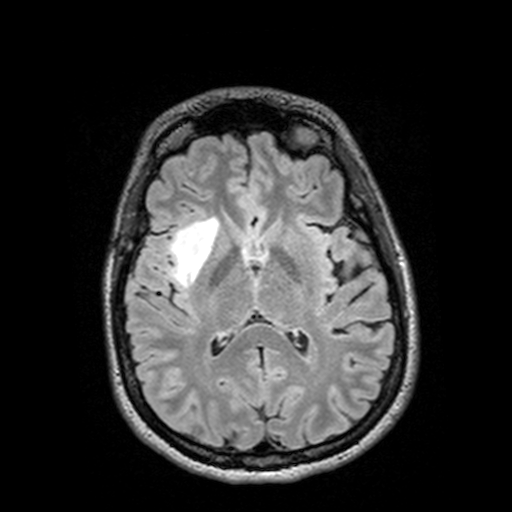
Brain MRI from a brain-tumour surgery series, one axial slice. Position 67 of 144 along the scan axis. T2 FLAIR. 1 mm slice thickness. 512 × 512 image matrix, field of view 250 × 250 mm. From the clinical record (not read from this slice): histopathology: Astrocytoma; WHO grade: 3; IDH mutation: yes; tumour location: Right Insular Temporal.
Structures marked on this image (expert manual segmentation):
- tumour: bounding box [x1, y1, x2, y2] px = [126, 217, 232, 288]